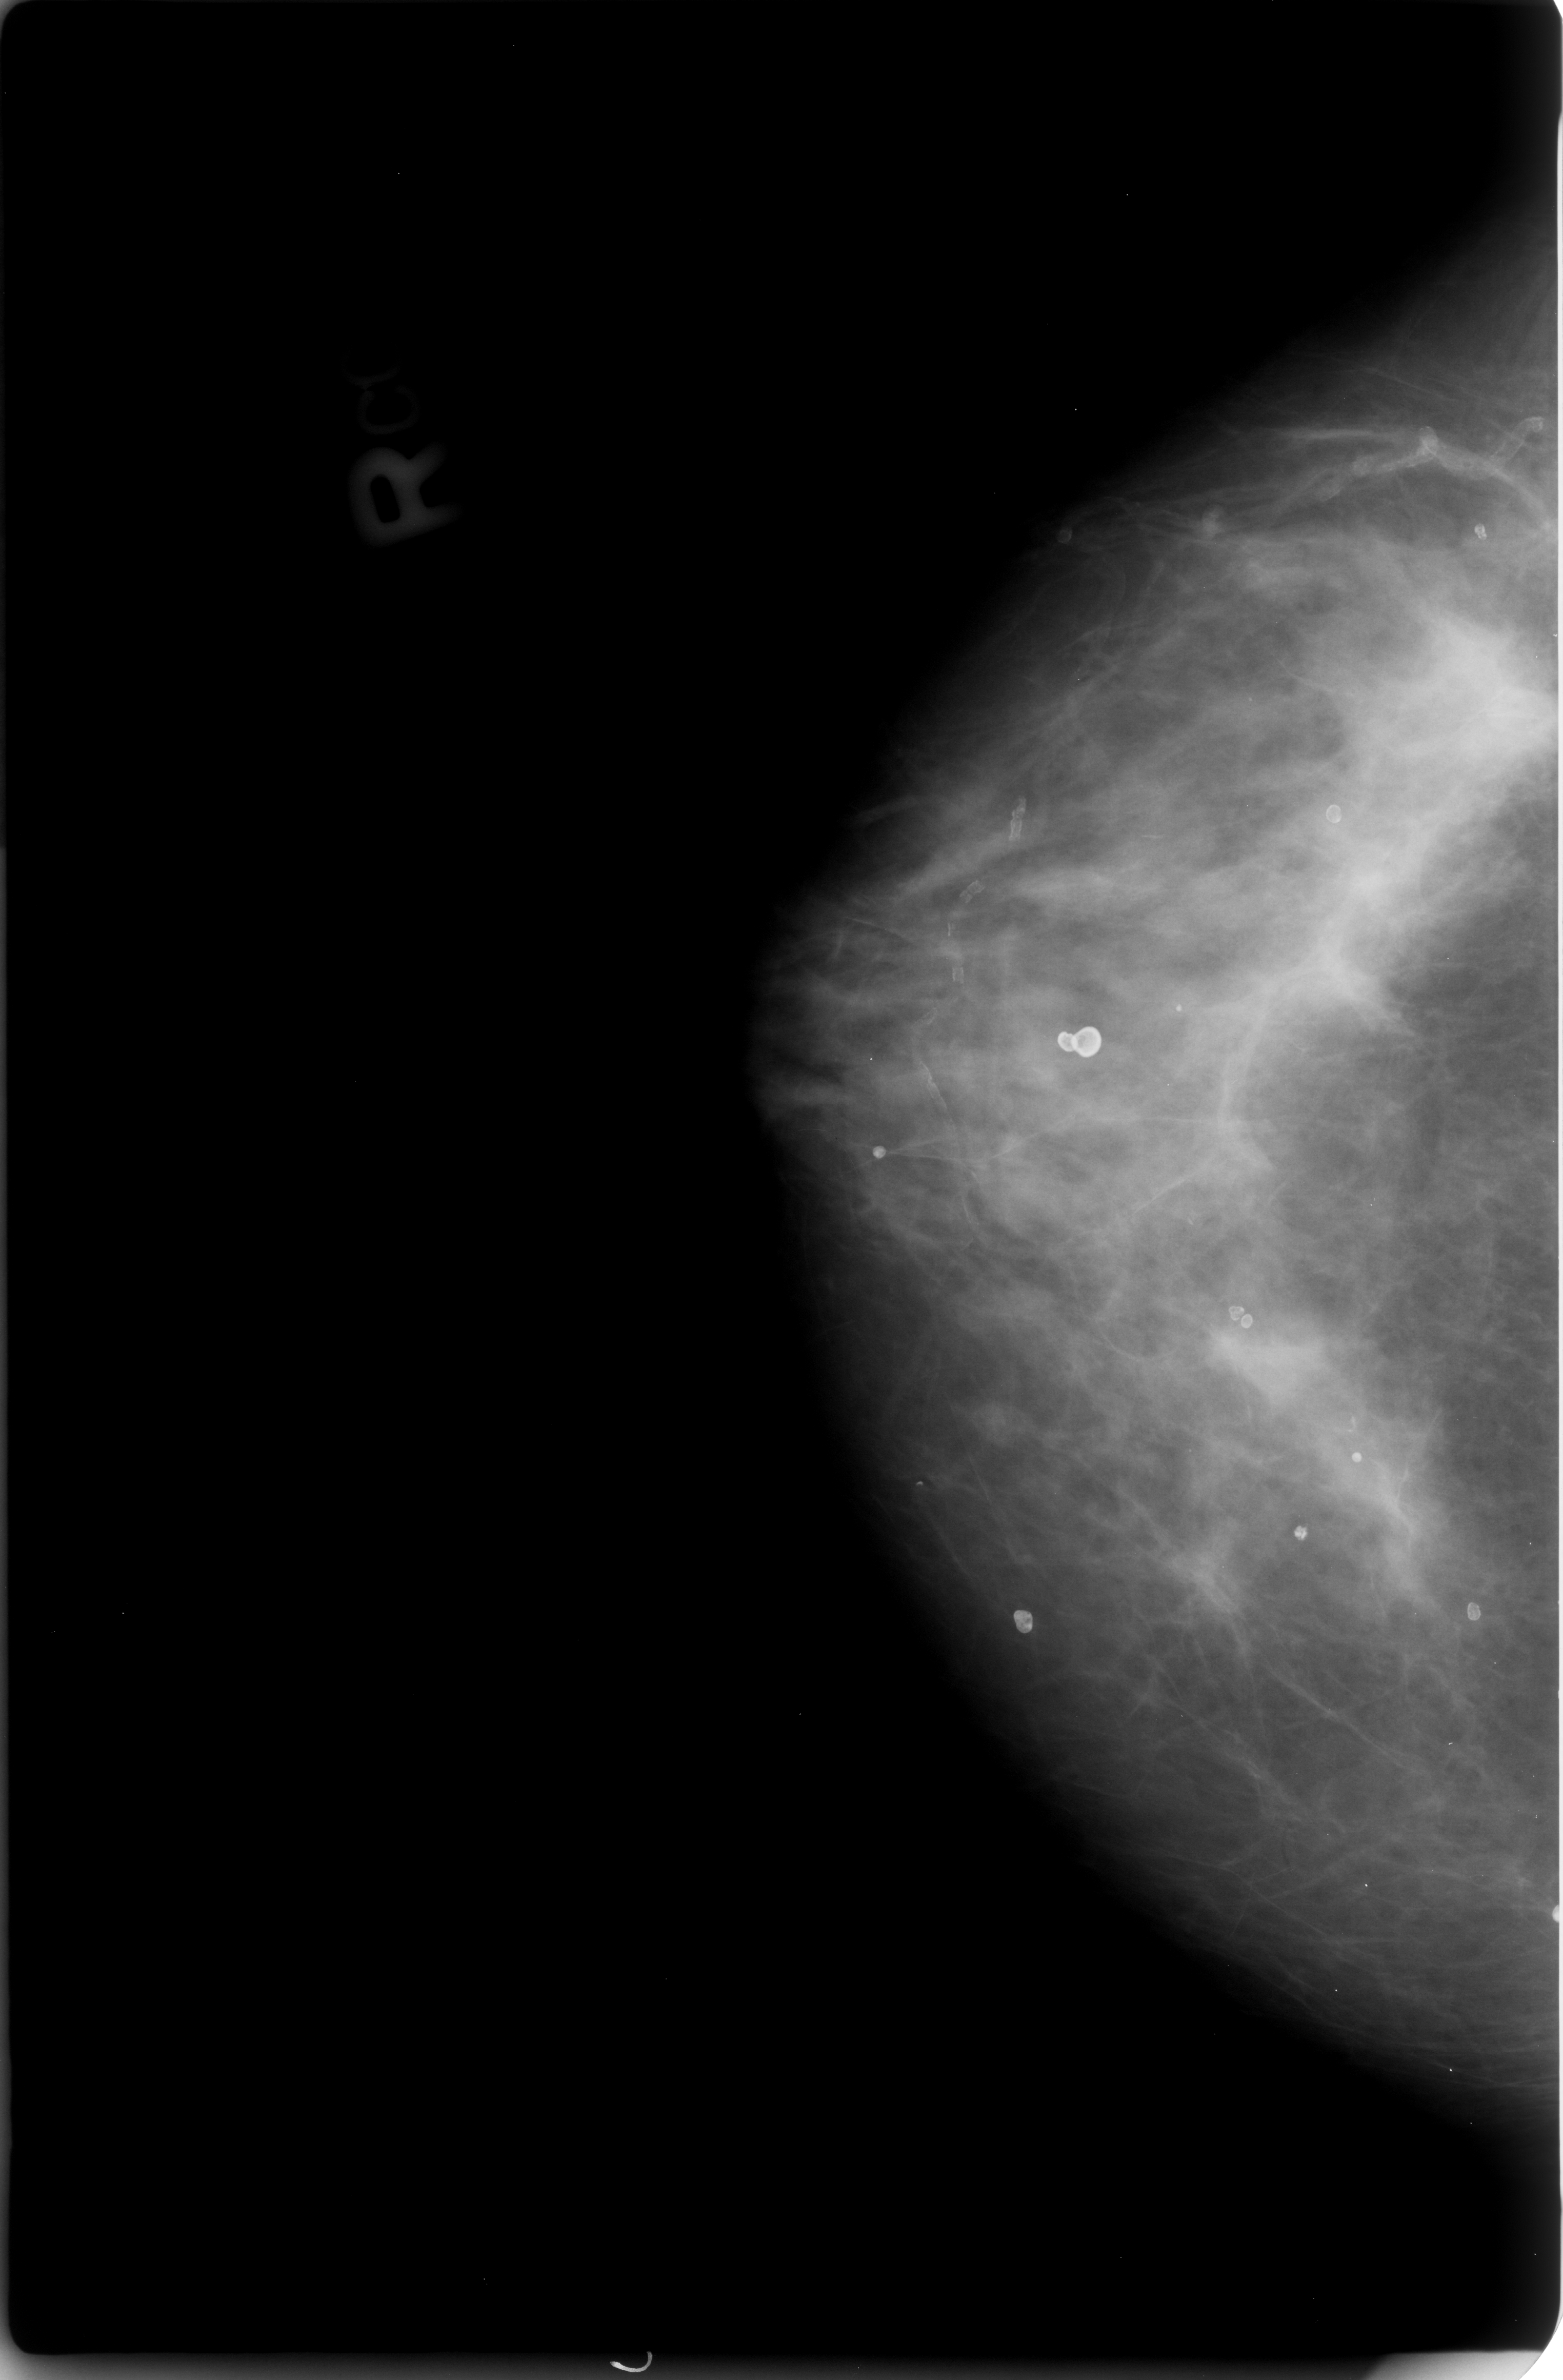
Mammogram (digitized film); right breast; CC view; breast composition: heterogeneously dense (BI-RADS density category 3 of 4).
Mass, shape irregular, margins obscured / ill defined; BI-RADS assessment category 4; subtlety rating 3 on a 1 (subtle) to 5 (obvious) scale; pathology result (as recorded, not read from the image): benign.